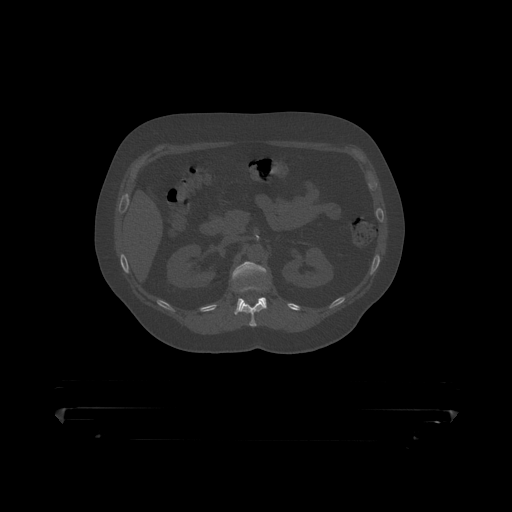
CT including the spine, one axial slice. Position 158 of 390 along the scan axis. Bone window (W 1800 / L 400 HU). 1.25 mm slice thickness. 512 × 512 image matrix, field of view 650 × 650 mm. Male patient, age 60 years. Case-level facts recorded for this patient, not image findings: primary cancer: prostate.
Annotated regions visible in this slice (semi-automatically segmented with operator editing):
- L1 vertebra: bounding box [x1, y1, x2, y2] px = [232, 262, 268, 315]
- T12 vertebra: [240, 300, 266, 319]